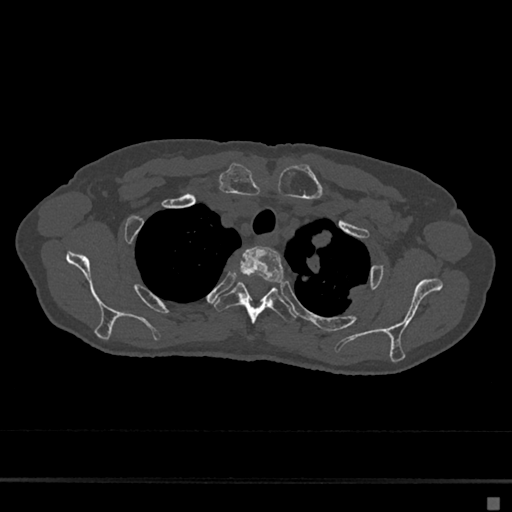
CT including the spine, one axial slice; reconstruction kernel Br40s/3; 120 kVp; bone window (W 1800 / L 400 HU); 0.5 mm slice thickness; 512 × 512 image matrix, field of view 360 × 360 mm. Patient: female, 68 years. Case-level facts recorded for this patient, not image findings: primary cancer: renal.
Annotated regions visible in this slice (semi-automatic segmentation, software-assisted and operator-edited):
- T2 vertebra: box from (x=235, y=246) to (x=284, y=283) px
- T3 vertebra: (x=214, y=282)–(x=296, y=324)